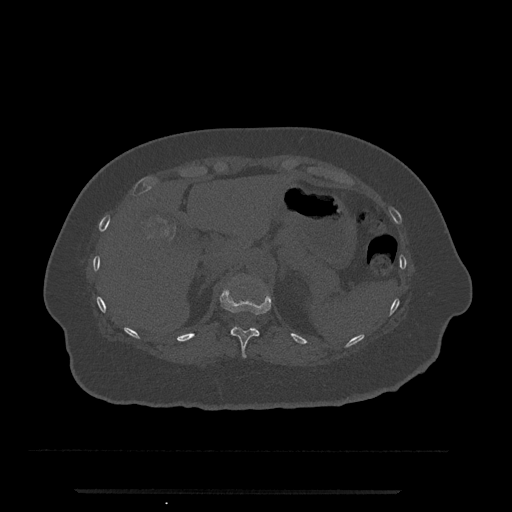
CT including the spine, one axial slice. Position 214 of 797 along the scan axis. Reconstruction kernel Br40s/3. 120 kVp. Bone window (W 1800 / L 400 HU). 0.5 mm slice thickness. 512 × 512 image matrix, field of view 440 × 440 mm. Patient: female, 51 years. From the clinical record (not read from this slice): primary cancer: neuro; vertebrae with lytic lesions (as recorded): T8.
Structures marked on this image (semi-automatically segmented with operator editing):
- T11 vertebra: bounding box <220,289,271,358> (left, top, right, bottom; pixels)